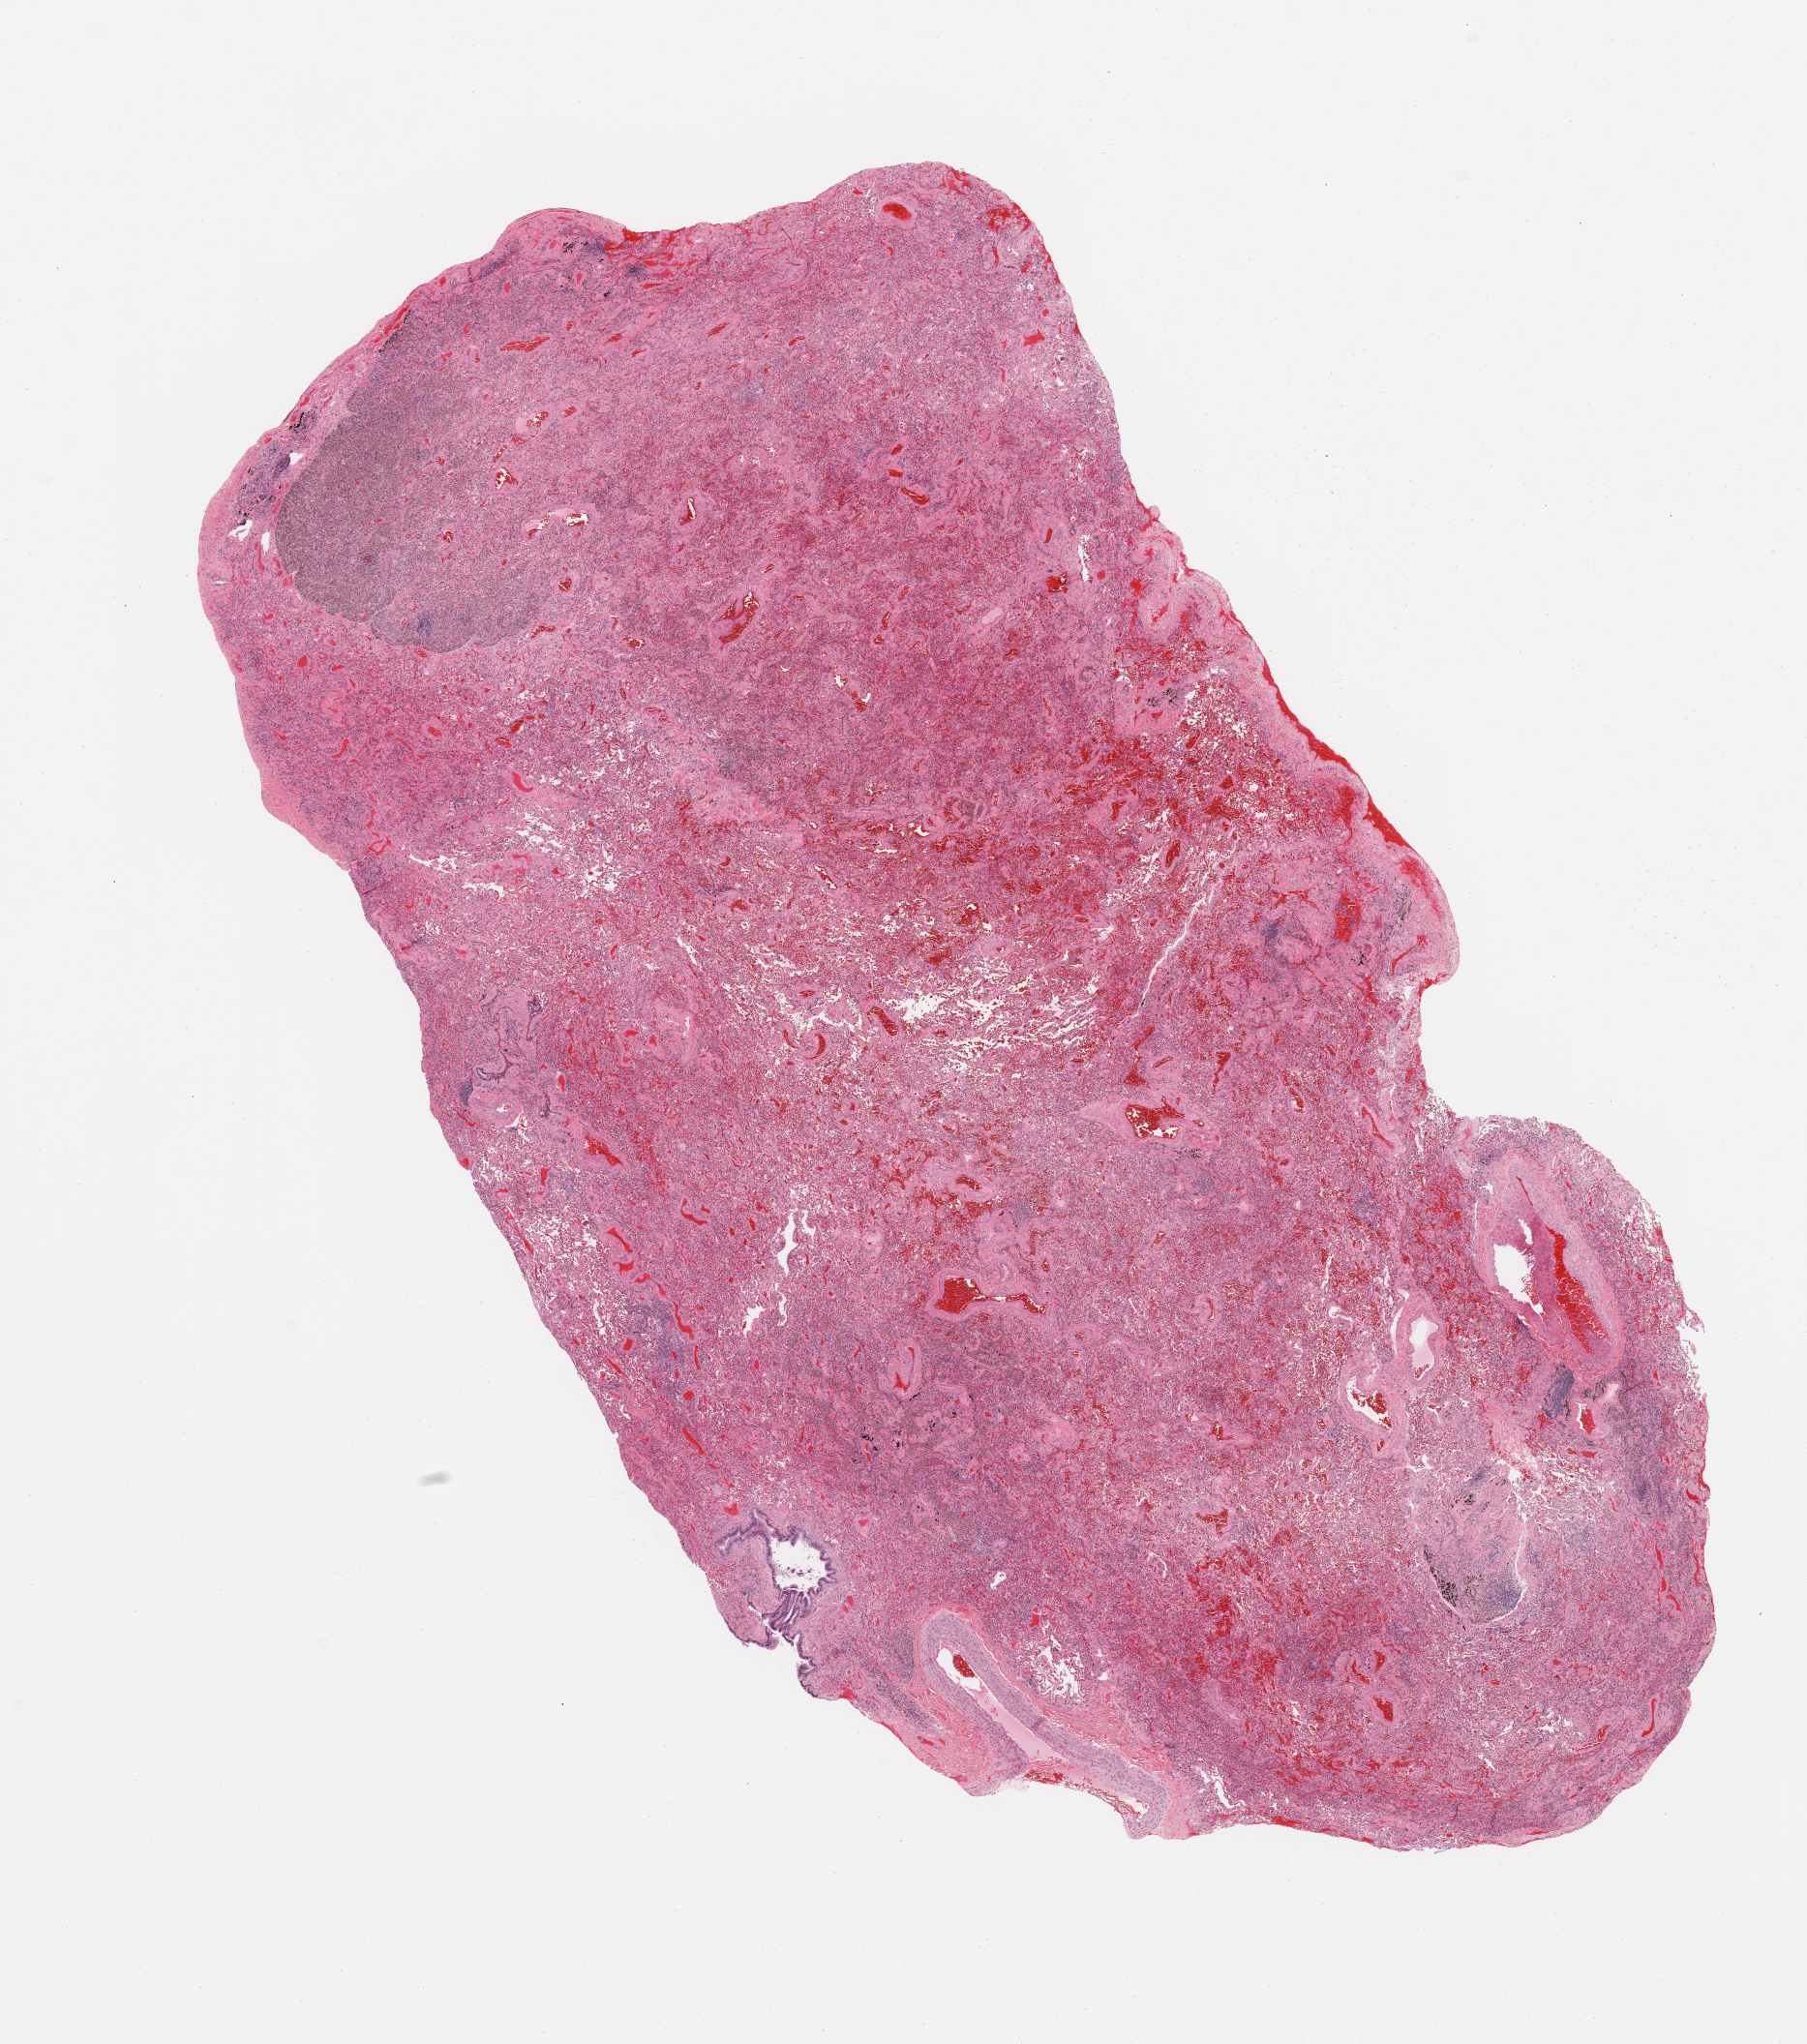
Whole-slide histology image, Hematoxylin and eosin (H&E) stained, shown as a low-resolution overview of the whole scanned area (about 14.8 x 16.7 mm), normal (non-tumour) tissue sample, sampled site: lung. Patient: female, age 56 years.
• this section: normal (non-tumour) tissue from the same patient
• patient diagnosis: Adenocarcinoma, NOS